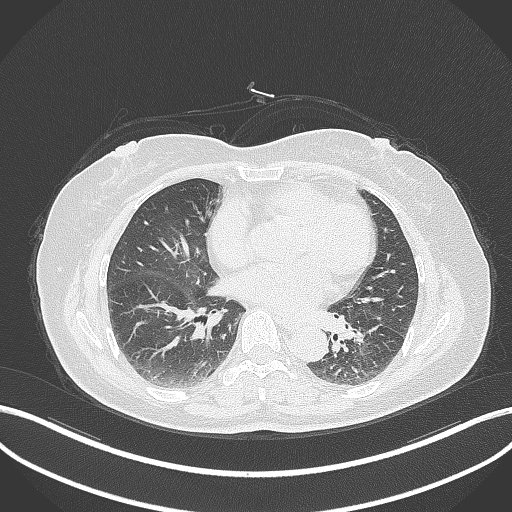
Chest CT, one axial slice; slice 167 of 311 in the series (ordered by position); reconstruction kernel B70f; 120 kVp; lung window (W 1500 / L -600 HU); 1 mm slice thickness; 512 × 512 image matrix, field of view 400 × 400 mm. Patient: female, 59 years. From the clinical record (not read from this slice): clinical TNM (as recorded): T2a N0 M0.
Outlined on this slice (rectangle marked by the reading radiologist):
- lung tumour (recorded histology: adenocarcinoma): bounding box [x1, y1, x2, y2] px = [350, 319, 384, 351]